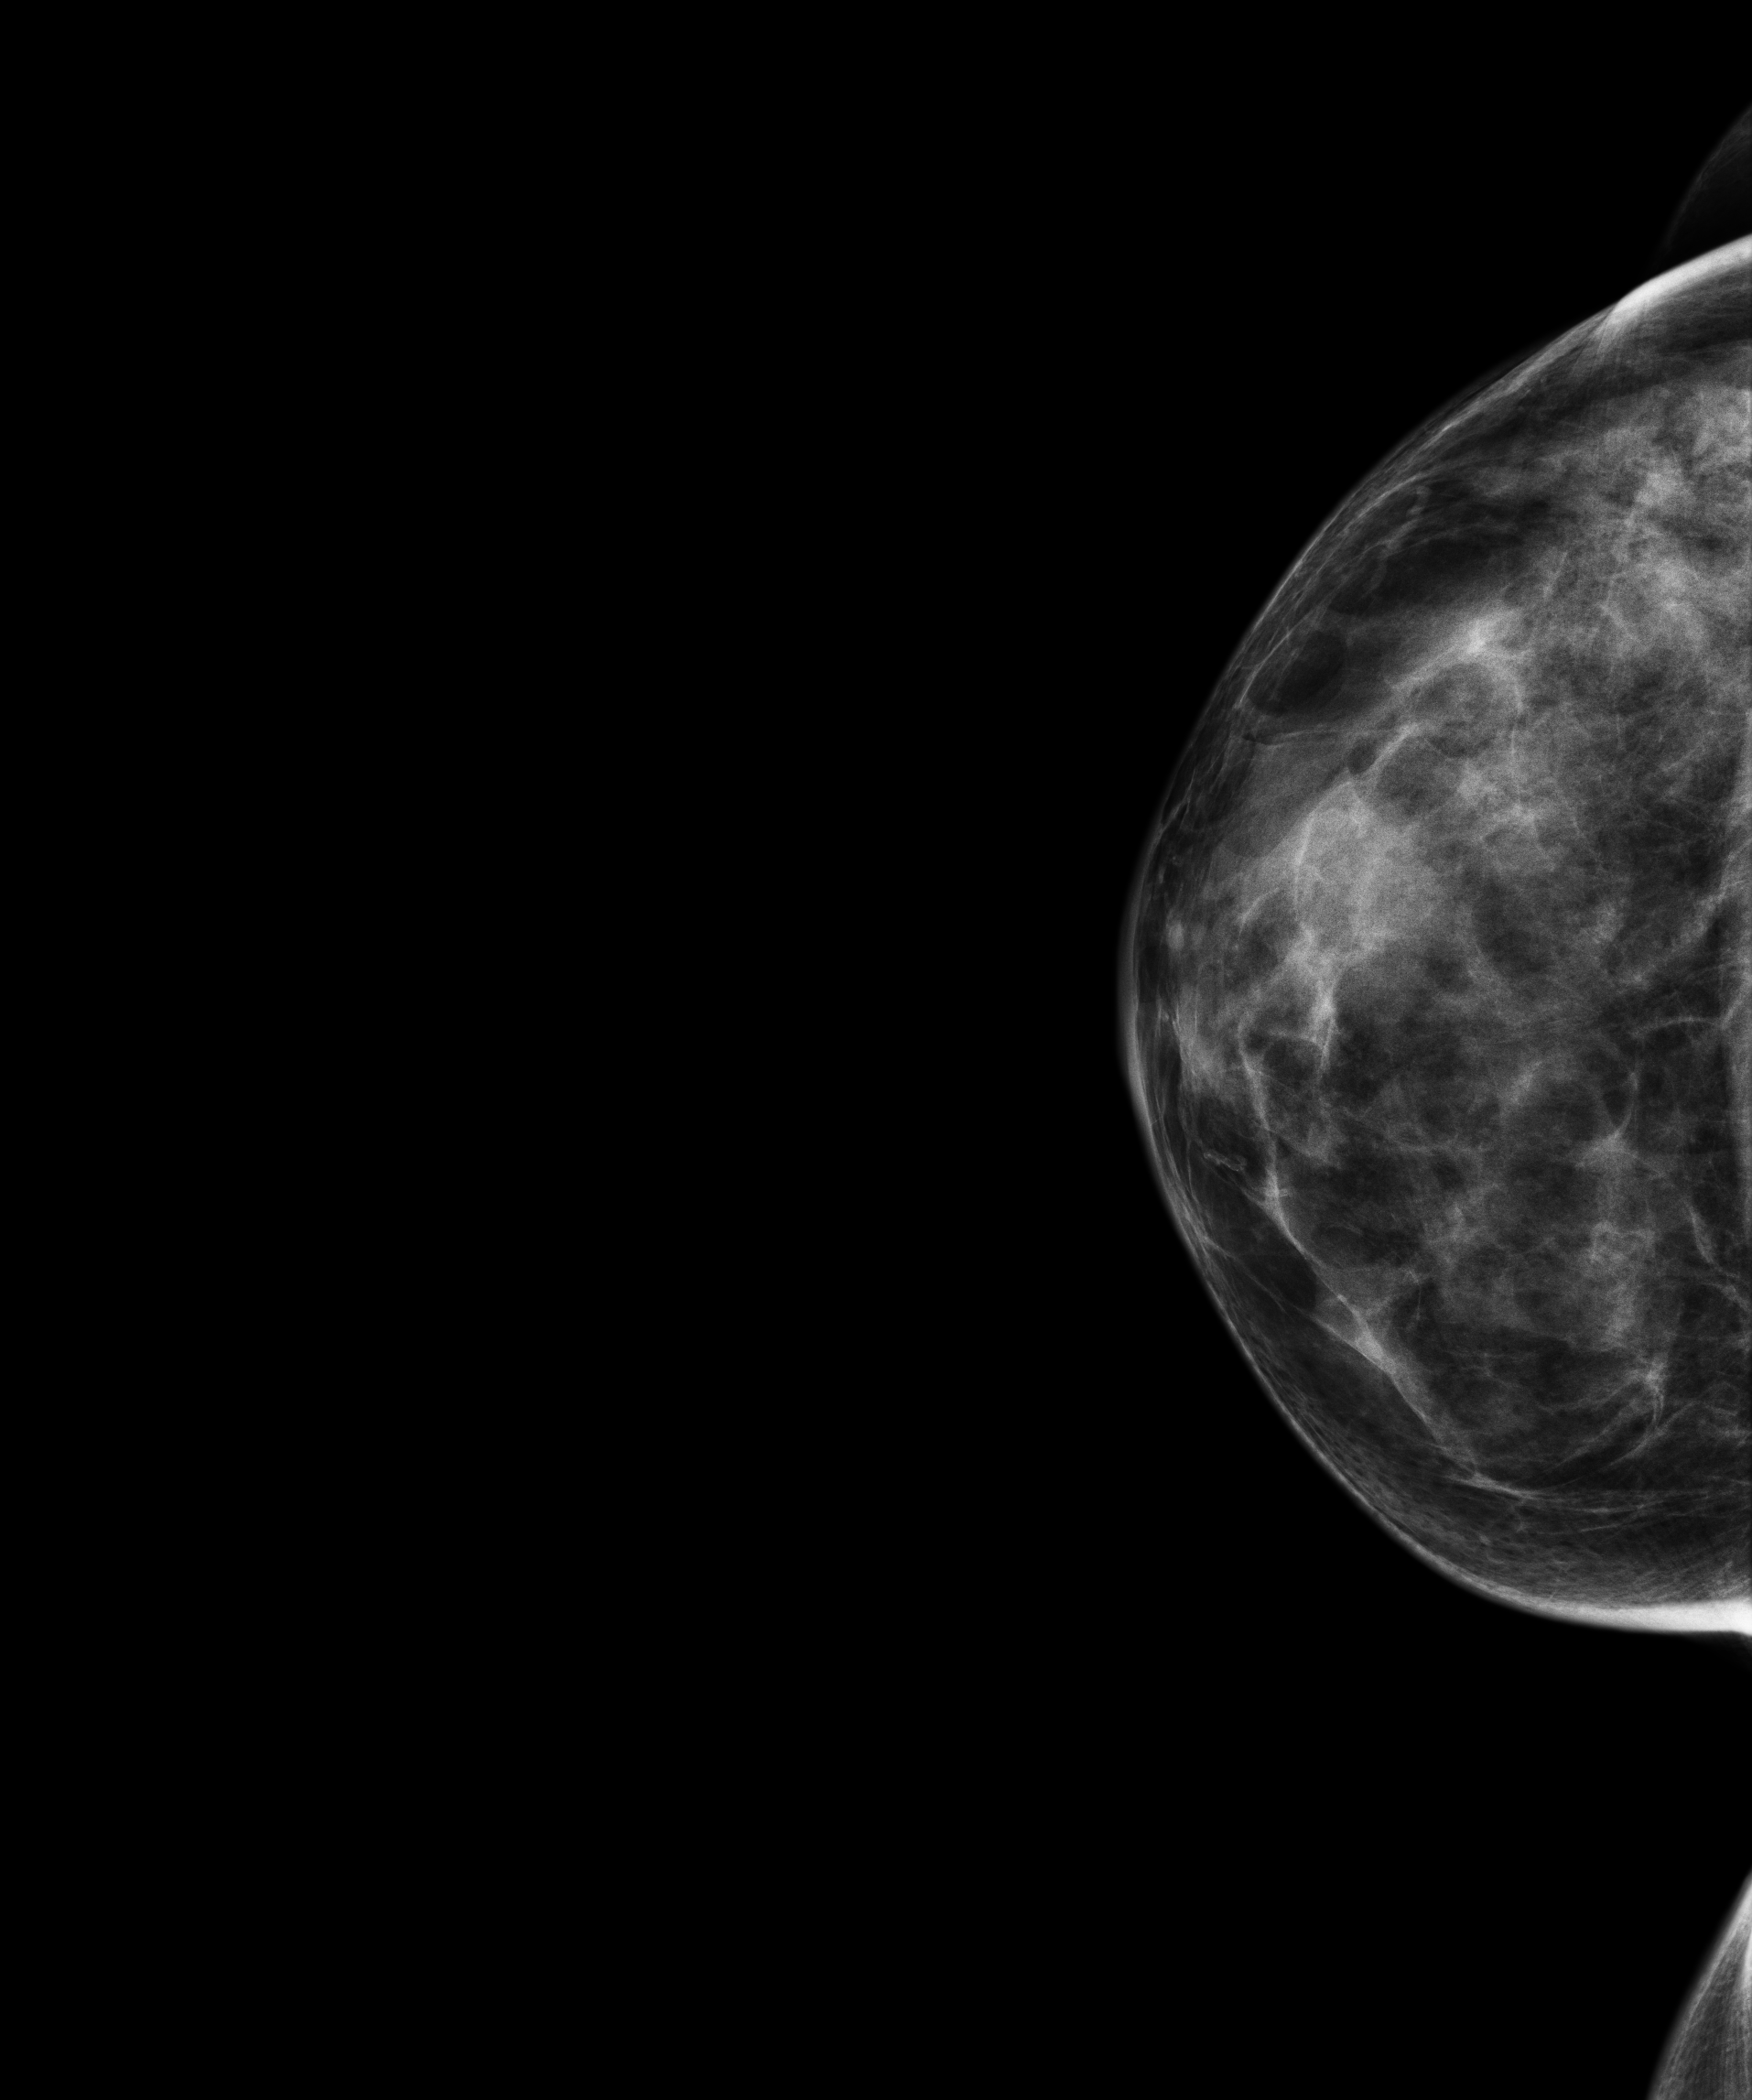
Digital mammogram (FFDM); right breast; cranio-caudal projection; annual screening mammography examination; compressed breast thickness 59 mm. Patient: female, 66 years.
BI-RADS breast density category at the screening exam (both breasts, scale 1–4): 3. Final BI-RADS assessment for this screening round (tomosynthesis exam, both breasts): category 1. Recall: no recall after this screen.